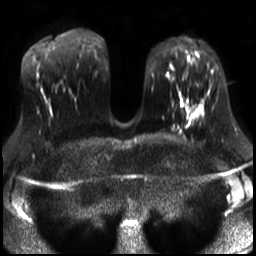
Breast MRI, one axial slice. Slice 14 of 30 in the series (ordered by position). Diffusion-weighted series; image 2 of 4 stored at this slice position (different b-values; order by instance number). 3 T. 256 × 256 image matrix, field of view 320 × 320 mm. Female patient.
Structures marked on this image (outlined manually by an expert reader):
- tumour on diffusion-weighted imaging: bounding box (x1, y1, x2, y2) in pixels: (194, 108, 200, 114)